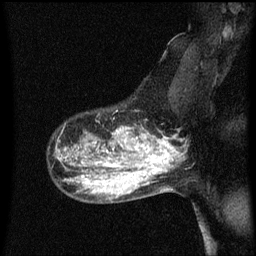
Breast MRI (dynamic contrast-enhanced), one sagittal slice; dynamic contrast-enhanced series, image 2 of 3 at this slice position (ordered by acquisition); 1.5 T; TE 4.2 ms, TR 8.4 ms; 2 mm slice thickness; 256 × 256 image matrix. Patient: female, 50 years.
Outlined on this slice (semi-automatic segmentation, software-assisted and operator-edited):
- analysis volume of interest (the breast-tissue region the enhancement analysis was run in; not a lesion): bounding box (x1, y1, x2, y2) in pixels: (100, 126, 153, 171)
- tumour enhancement mask (voxels above the 70 % enhancement threshold inside the analysis volume of interest): (106, 128, 153, 171)